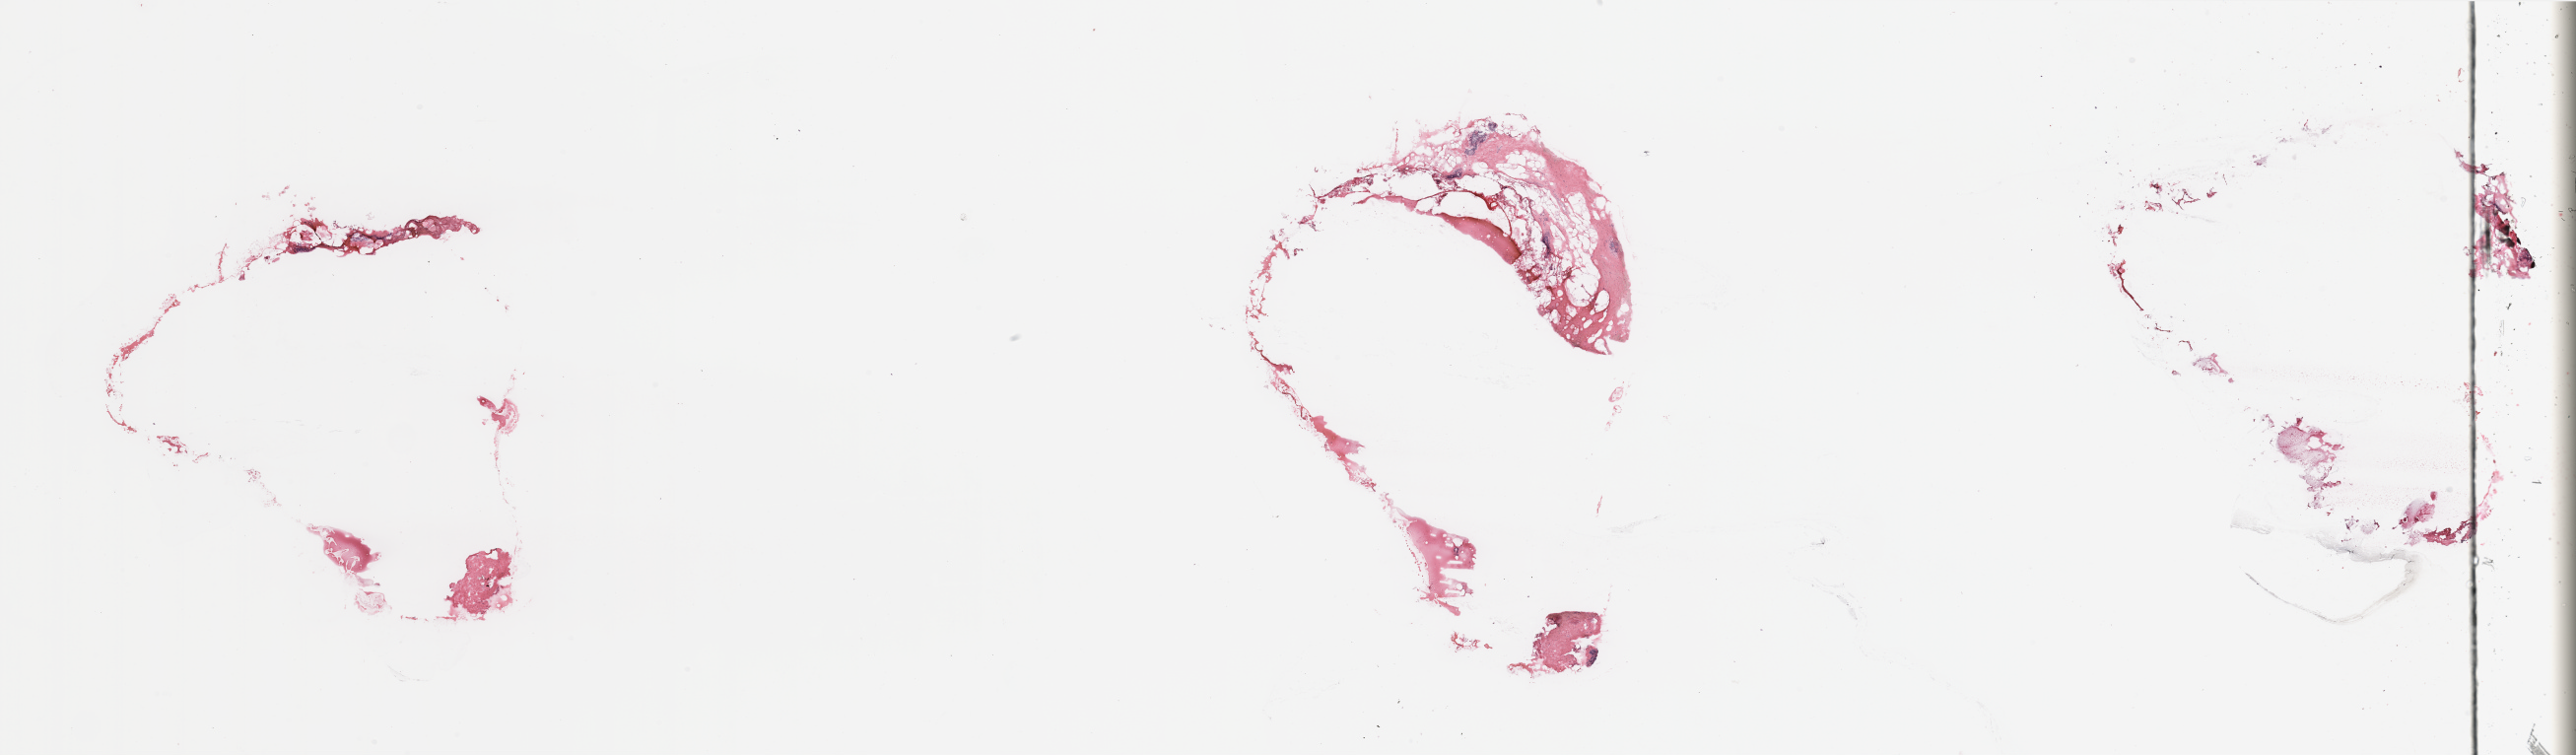
Whole-slide histology image, H&E-stained, whole scanned area (about 41.3 x 12.1 mm) shown as a low-resolution overview. Breast, tissue type not recorded.
Patient diagnosis (cohort enrolment): breast cancer (breast).